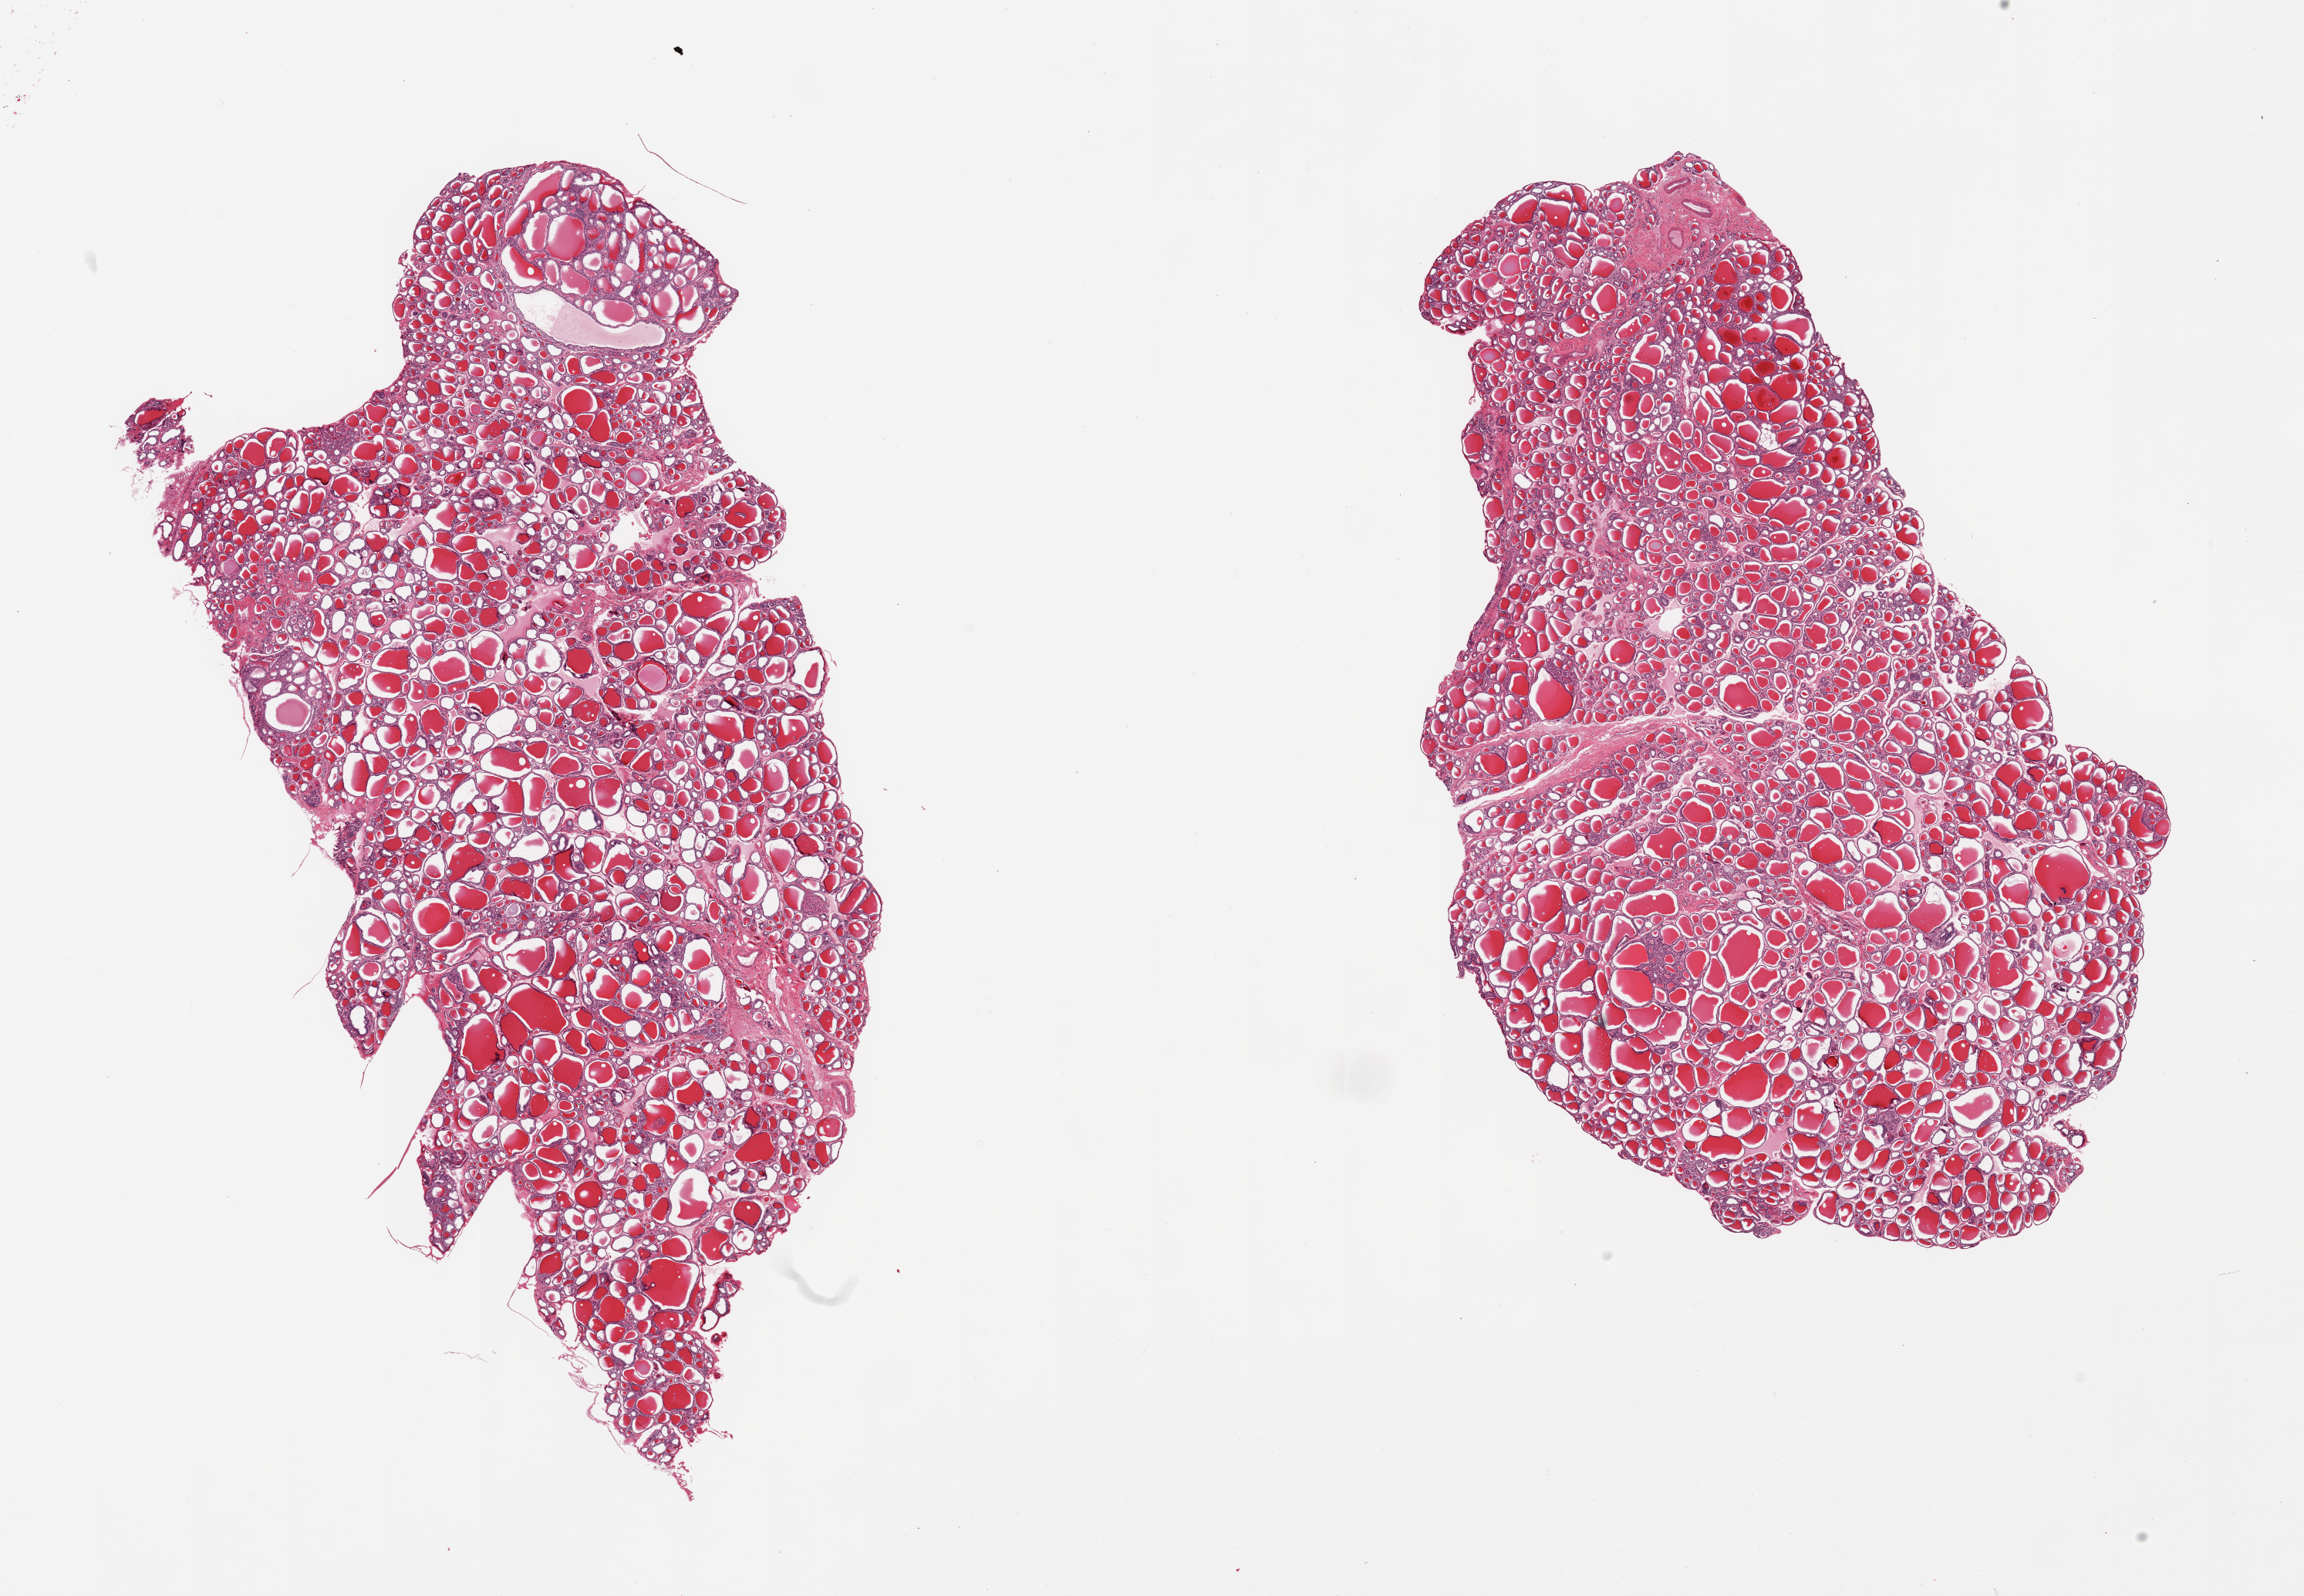
Hematoxylin and eosin (H&E) whole-slide image, brightfield — low-resolution overview of the scanned area, about 23.6 x 16.4 mm (slide scanned at 20x), PAXgene-fixed paraffin-embedded (PFPE) section, sampled site (target tissue): thyroid, tissue donor sample. Female donor.
Pathologist's review note for this sample: 2 pieces, no abnormalities.